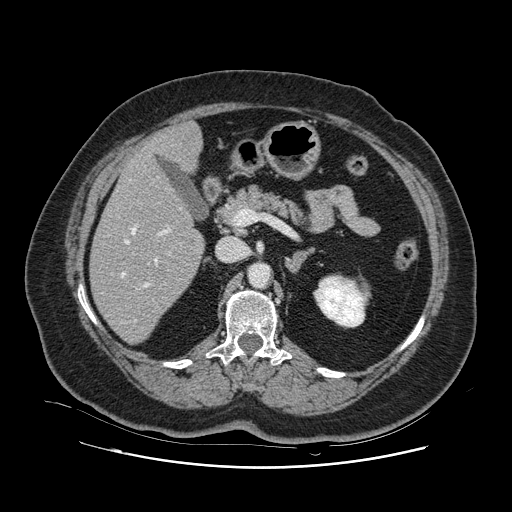
Contrast-enhanced abdominal CT, one axial slice; position 53 of 132 along the scan axis; 120 kVp; intravenous contrast given; soft-tissue window (W 400 / L 40 HU); 512 × 512 image matrix, field of view 391 × 391 mm. Female patient, age 73 years. From the clinical record (not read from this slice): diagnosis: colorectal cancer liver metastases, imaged before liver resection; multiple liver metastases: no; largest metastasis: 7 cm; disease in both lobes: no.
Structures marked on this image (outlined manually by an expert reader):
- hepatic veins: bounding box <121,177,181,321> (left, top, right, bottom; pixels)
- liver: <91,124,204,343>
- planned liver remnant (the part of the liver to remain after resection): <91,147,204,343>
- portal vein (with intrahepatic branches): <144,228,170,287>